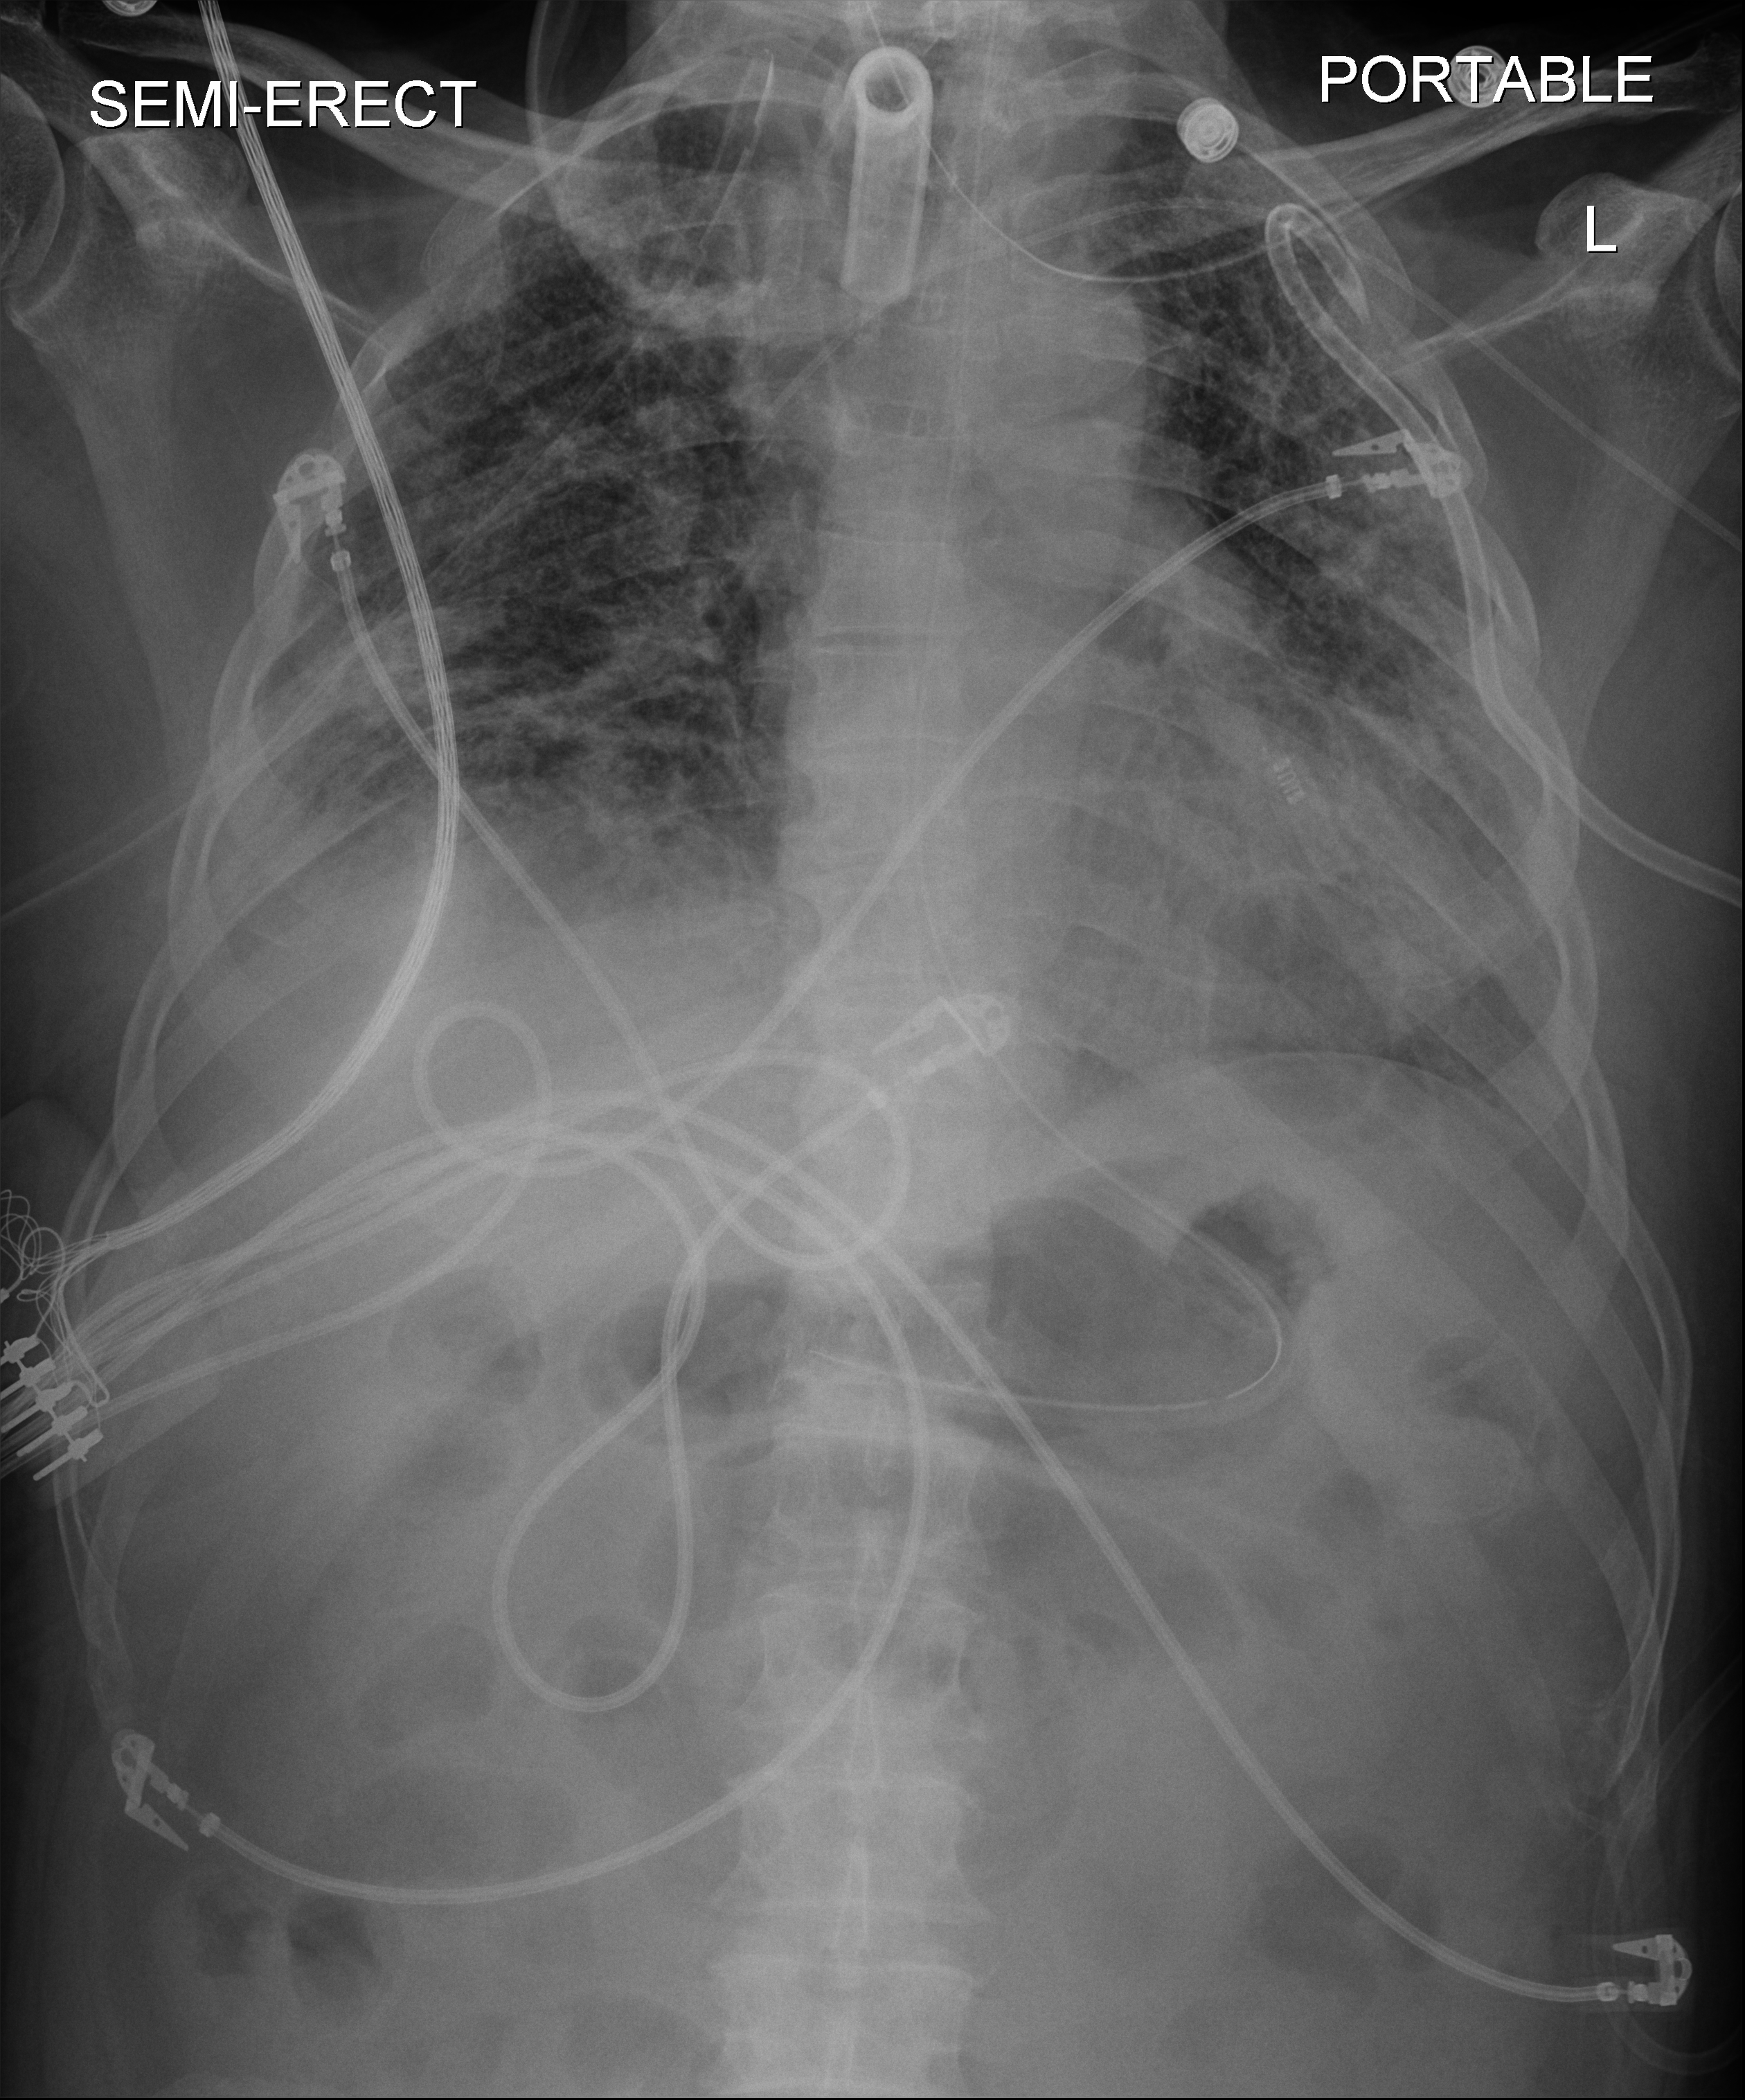
Bedside chest radiograph (digital radiography). Patient hospitalised with COVID-19; male, aged 18–59 years.
From the hospital-stay record, not from the radiograph (when in the stay this image was taken is not recorded):
- admitted to intensive care during this hospital stay: yes
- mechanically ventilated during this hospital stay: yes